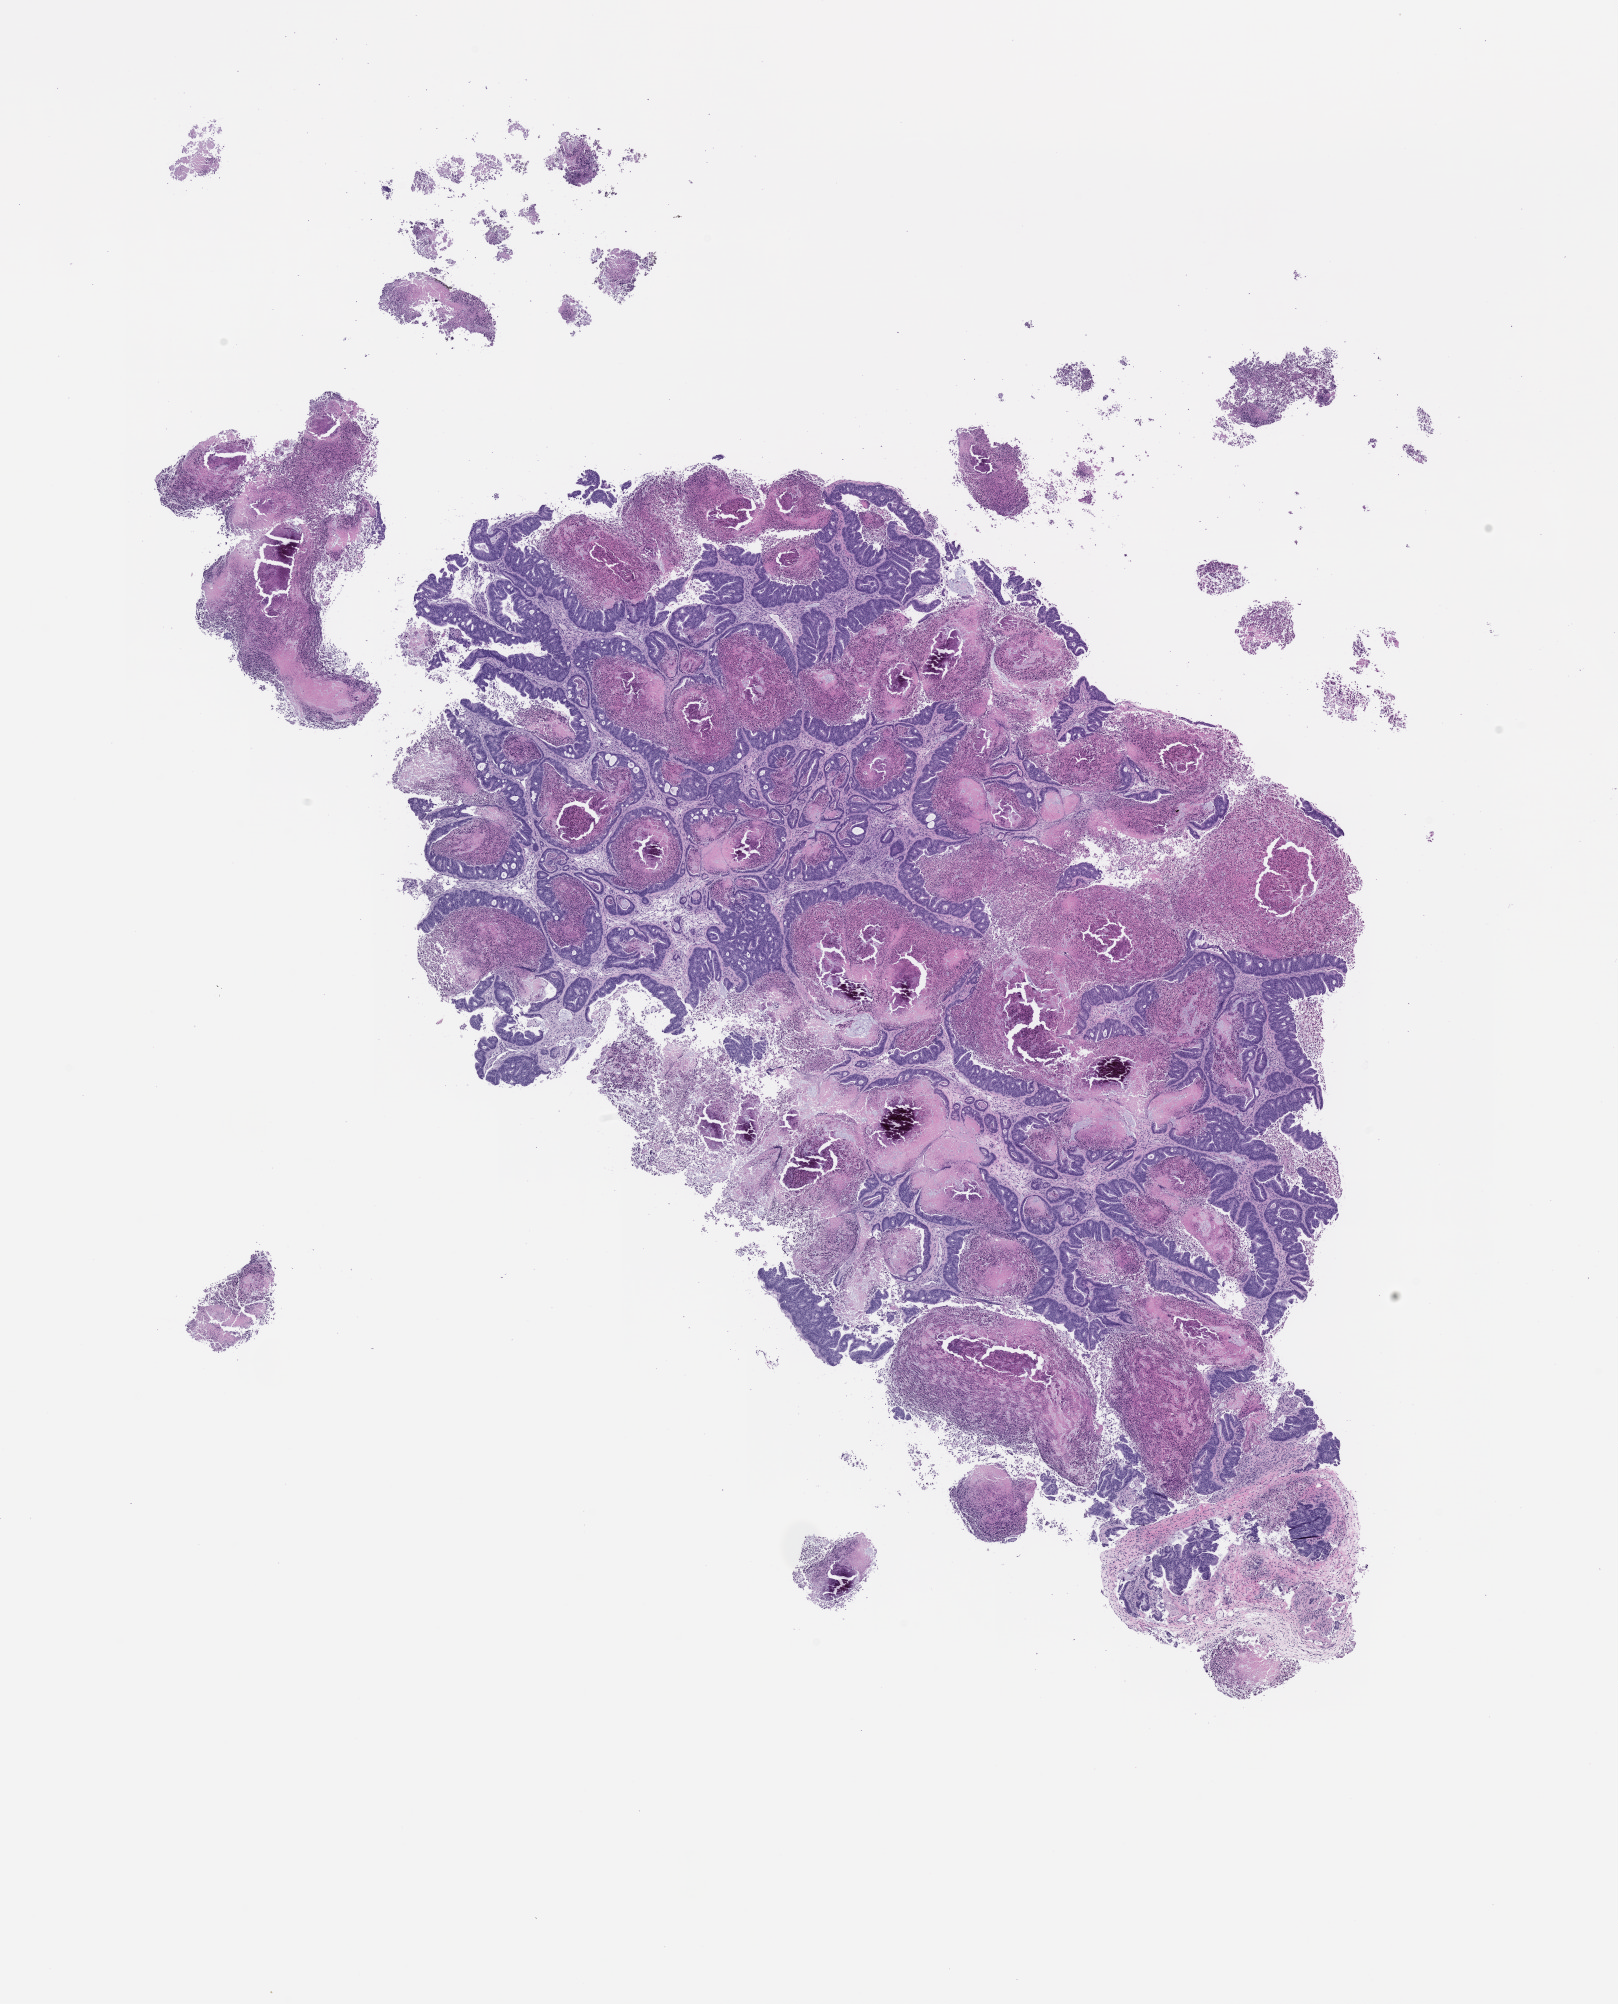
Hematoxylin and eosin (H&E) whole-slide image of a patient-derived xenograft (PDX) tumor grown in a mouse, passage 1 — low-resolution overview of the scanned area, about 13.0 x 16.1 mm. Formalin-fixed paraffin-embedded section. Tumor site category: rectum.
Originating patient diagnosis: Rectal Adenocarcinoma.